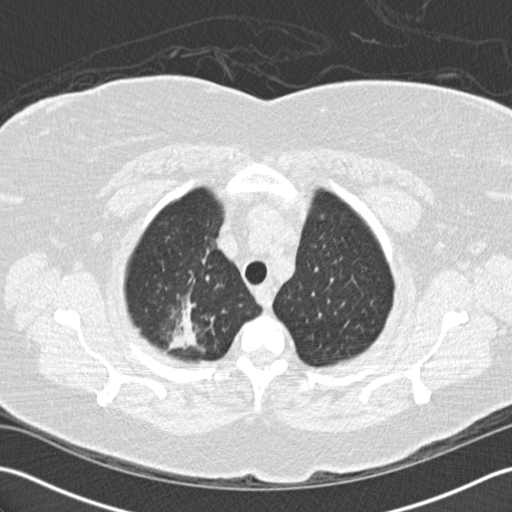
Chest CT (low-dose screening protocol), one axial image, first (baseline) screen, lung window (W 1500 / L -600 HU), 2 mm slice thickness, standard (soft-tissue) reconstruction kernel (B30f), slice 23 of 156 in the series. Female, age 72 years at enrolment. Former smoker at enrolment.
Lesion marked by an expert reader, bounding box [x1, y1, x2, y2] px = [136, 276, 227, 367]. The screening reader recorded 2 non-calcified nodules or masses ≥4 mm on this exam (right lower lobe, right lower lobe); which of them this box marks is not recorded. Participant outcome: lung cancer diagnosed 494 days after this screen (after the second annual screen) — bronchiolo-alveolar adenocarcinoma, NOS, right upper lobe, stage IIIB (AJCC 6th edition), 45 mm at pathology.